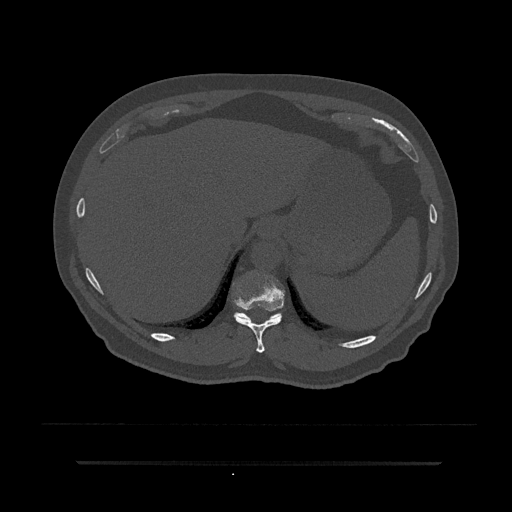
CT including the spine, one axial slice. Position 308 of 797 along the scan axis. 120 kVp. Bone window (W 1800 / L 400 HU). 0.5 mm slice thickness. 512 × 512 image matrix, field of view 464 × 464 mm. Male patient, age 59 years. From the clinical record (not read from this slice): primary cancer: bile ducts; vertebrae with lytic lesions (as recorded): T10.
Annotated regions visible in this slice (semi-automatic segmentation, software-assisted and operator-edited):
- T10 vertebra: bounding box [x1, y1, x2, y2] px = [233, 274, 285, 353]
- T11 vertebra: [234, 312, 282, 322]